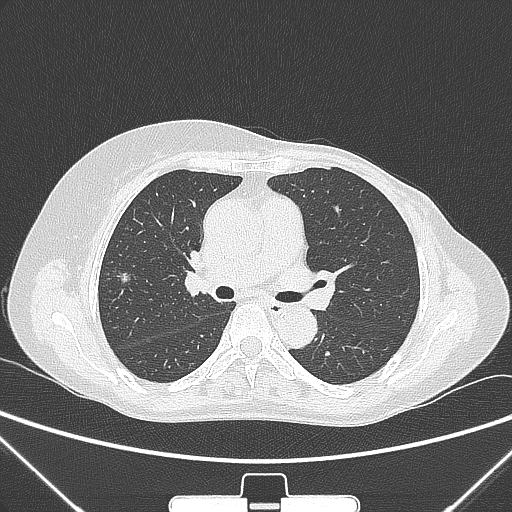
Chest CT, one axial slice. Slice 151 of 265 in the series (ordered by position). Lung window (W 1500 / L -600 HU). 512 × 512 image matrix, field of view 350 × 350 mm. Female patient, age 64 years. Case-level facts recorded for this patient, not image findings: clinical TNM (as recorded): T1c N0 M0; histopathological grade: G1-2.
Outlined on this slice (bounding box drawn by a radiologist):
- lung tumour (recorded histology: adenocarcinoma): bounding box (x1, y1, x2, y2) in pixels: (113, 268, 133, 289)